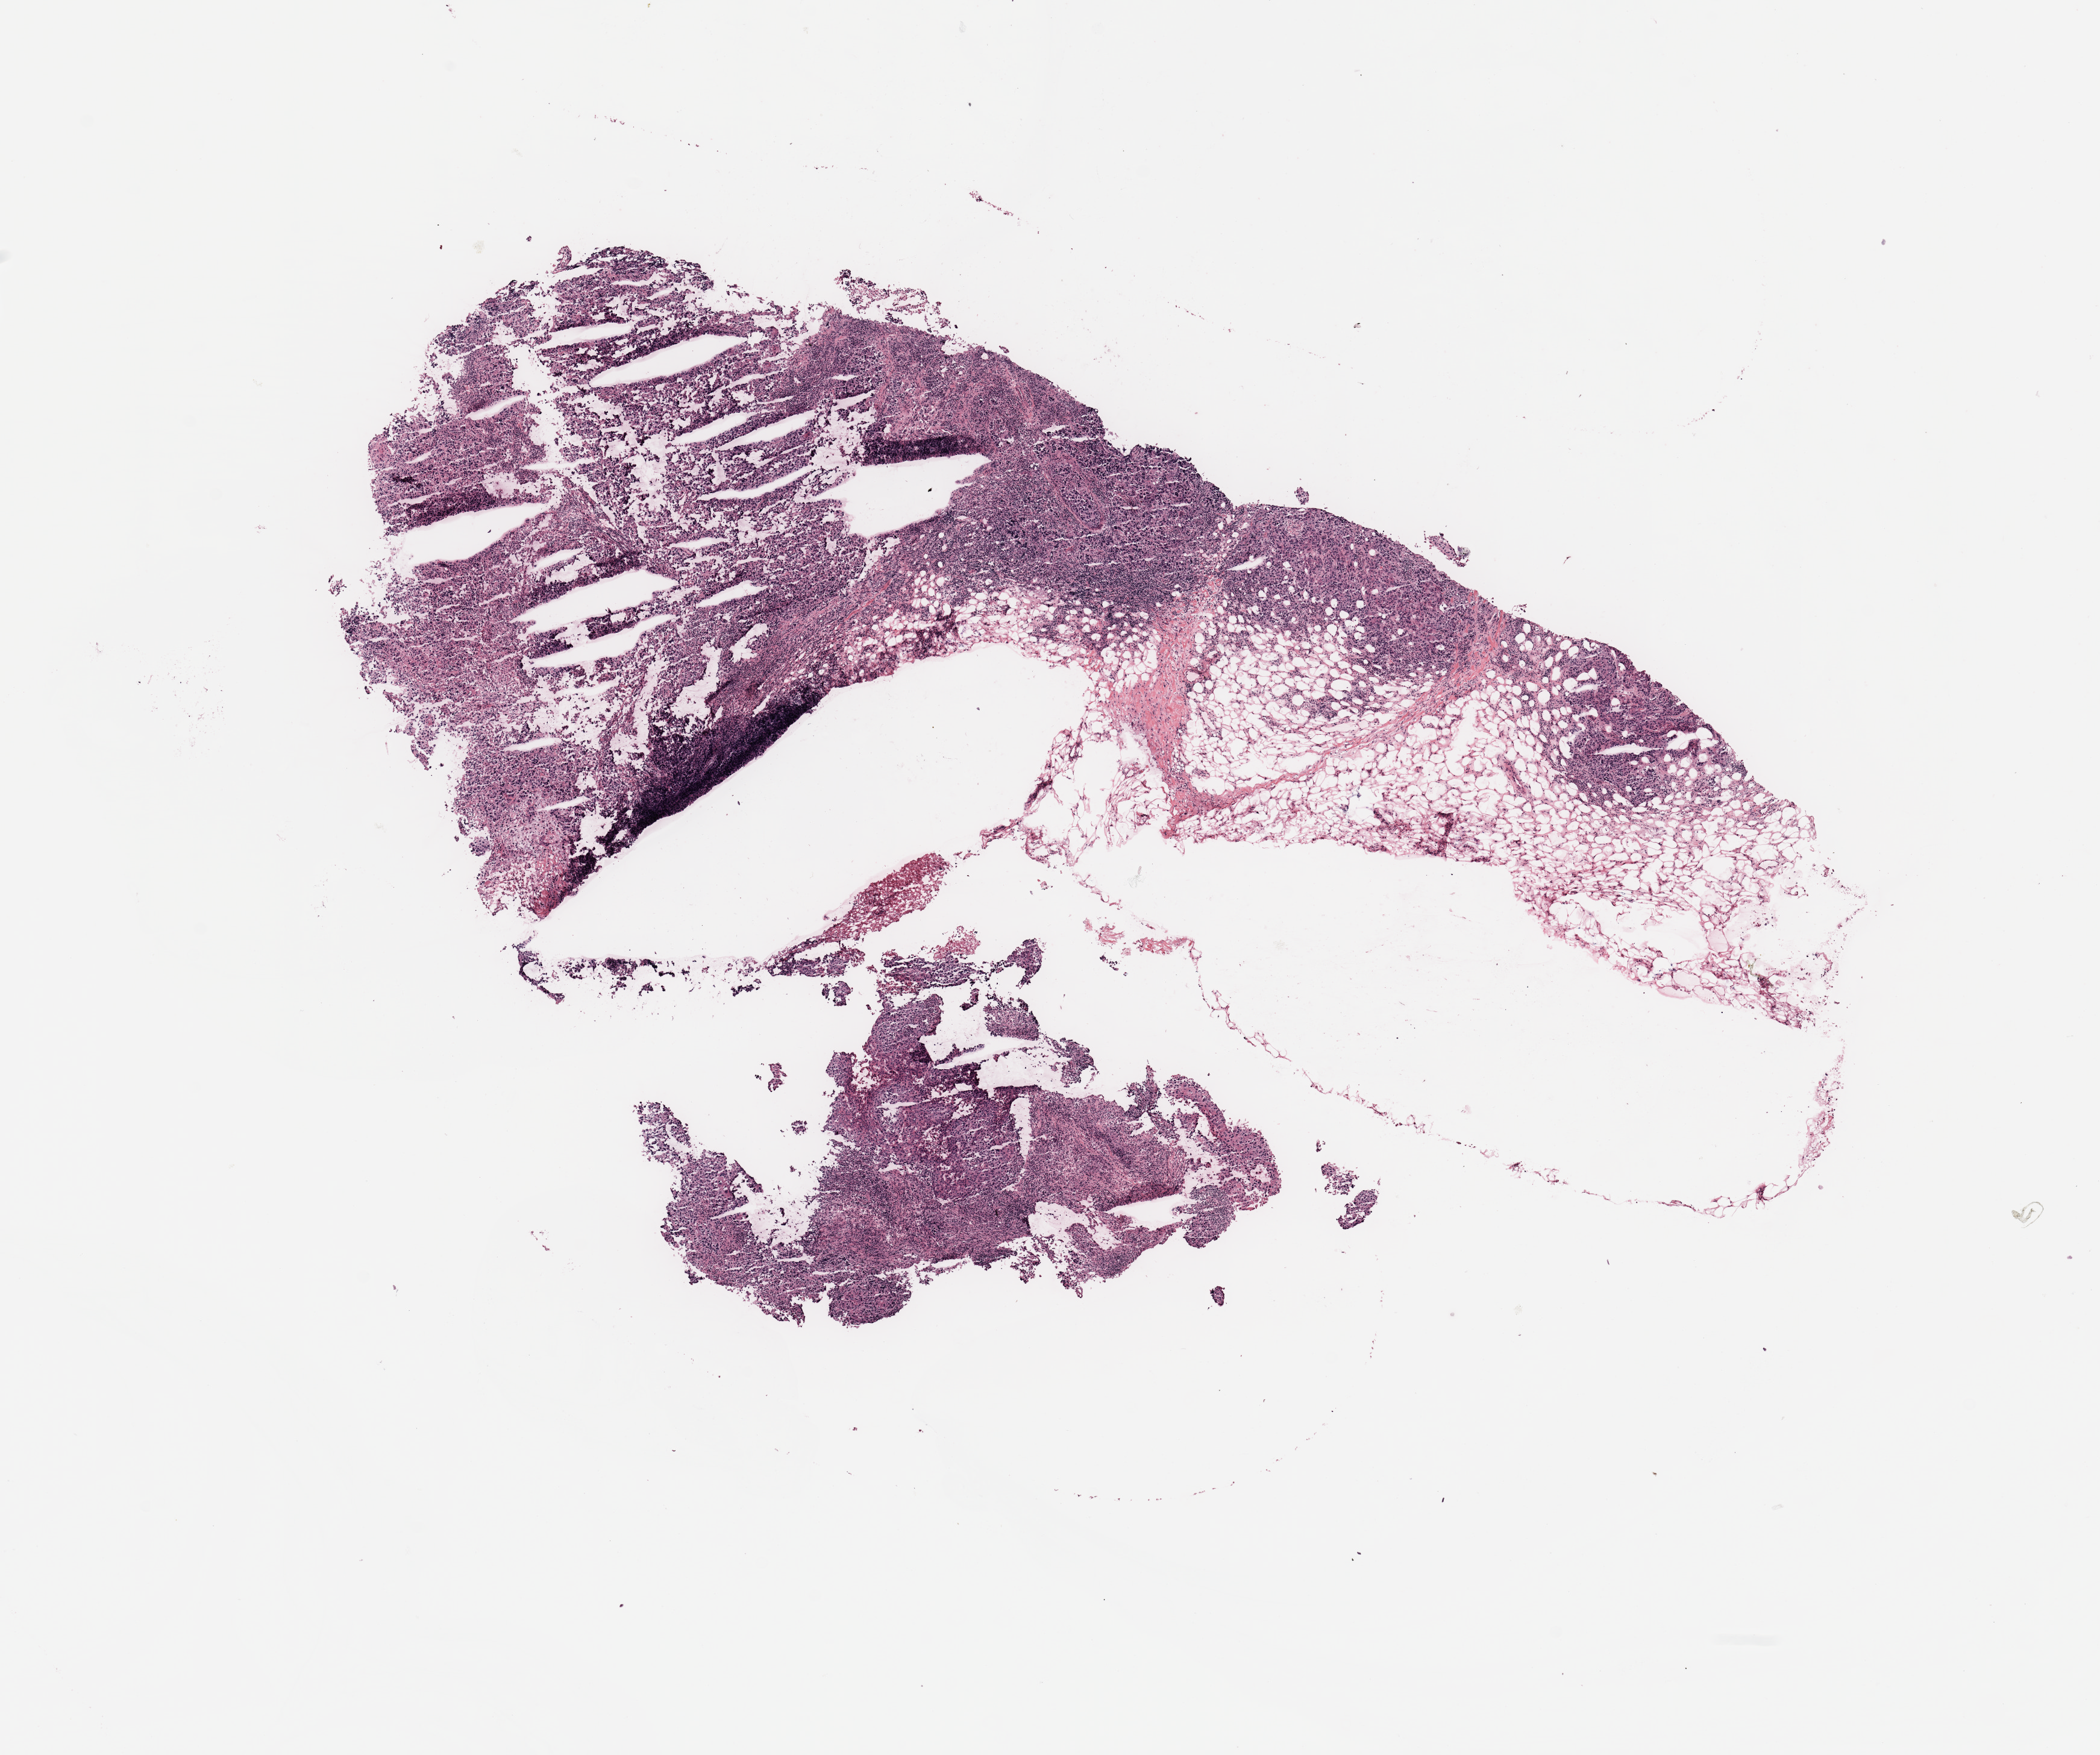
H&E-stained whole-slide image — shown as a low-resolution overview of the whole scanned area (about 13.8 x 11.5 mm, slide scanned at 20x). Tumour tissue sample, breast. 40-year-old female patient.
Histologic diagnosis: Infiltrating duct carcinoma, NOS. AJCC pathologic stage: IIB.